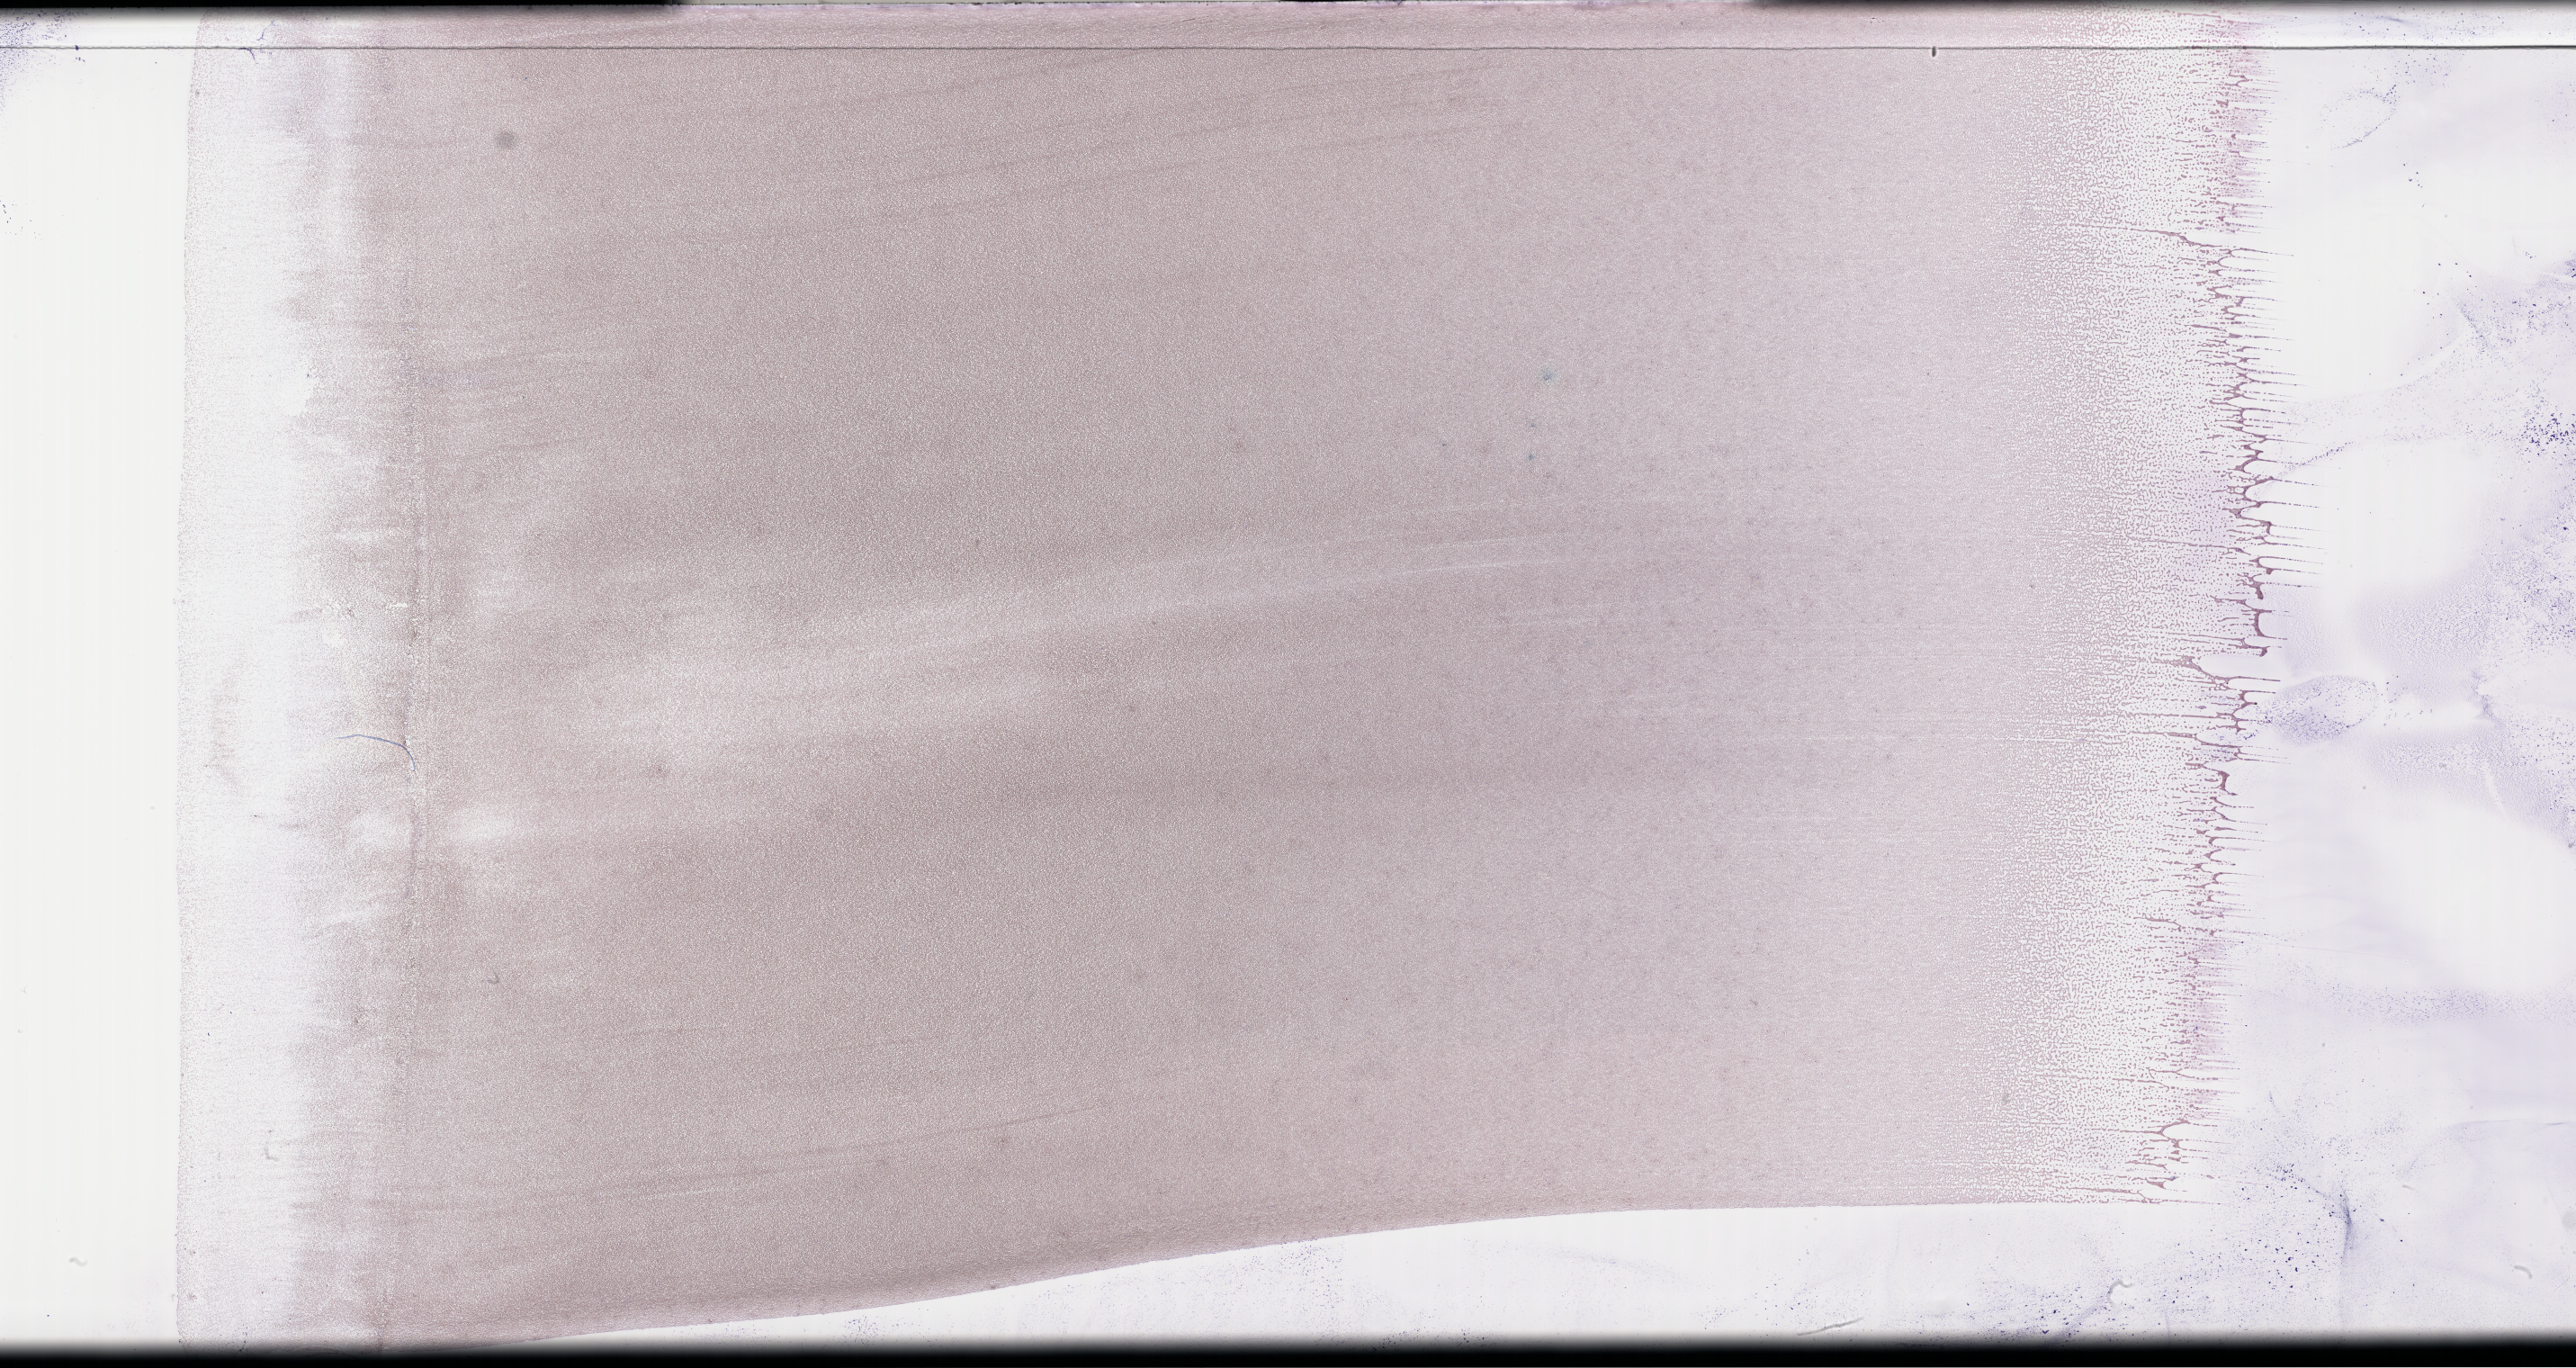
Whole-slide image of a whole blood smear, Wright–Giemsa stain — shown as a low-resolution overview of the whole scanned area (about 46.2 x 24.5 mm); specimen time point: collected on treatment. Female patient.
From a patient with: Plasma Cell Myeloma.